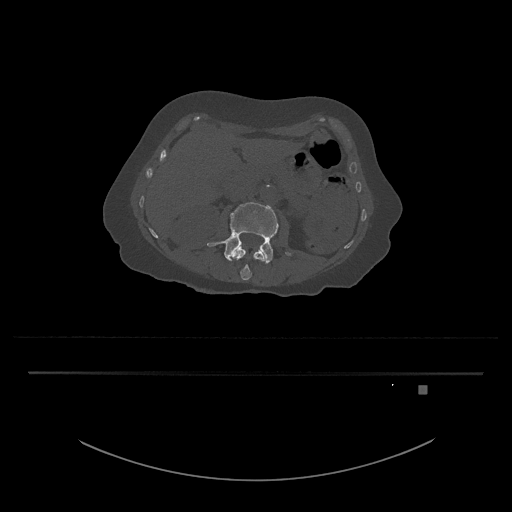
CT including the spine, one axial slice. Position 452 of 797 along the scan axis. Reconstruction kernel Br40s/3. 120 kVp. Bone window (W 1800 / L 400 HU). 0.5 mm slice thickness. 512 × 512 image matrix, field of view 500 × 500 mm. Female patient, age 57 years. Case-level facts recorded for this patient, not image findings: primary cancer: cervical.
Structures marked on this image (semi-automatic segmentation, software-assisted and operator-edited):
- L3 vertebra: bounding box [x1, y1, x2, y2] px = [207, 202, 291, 264]